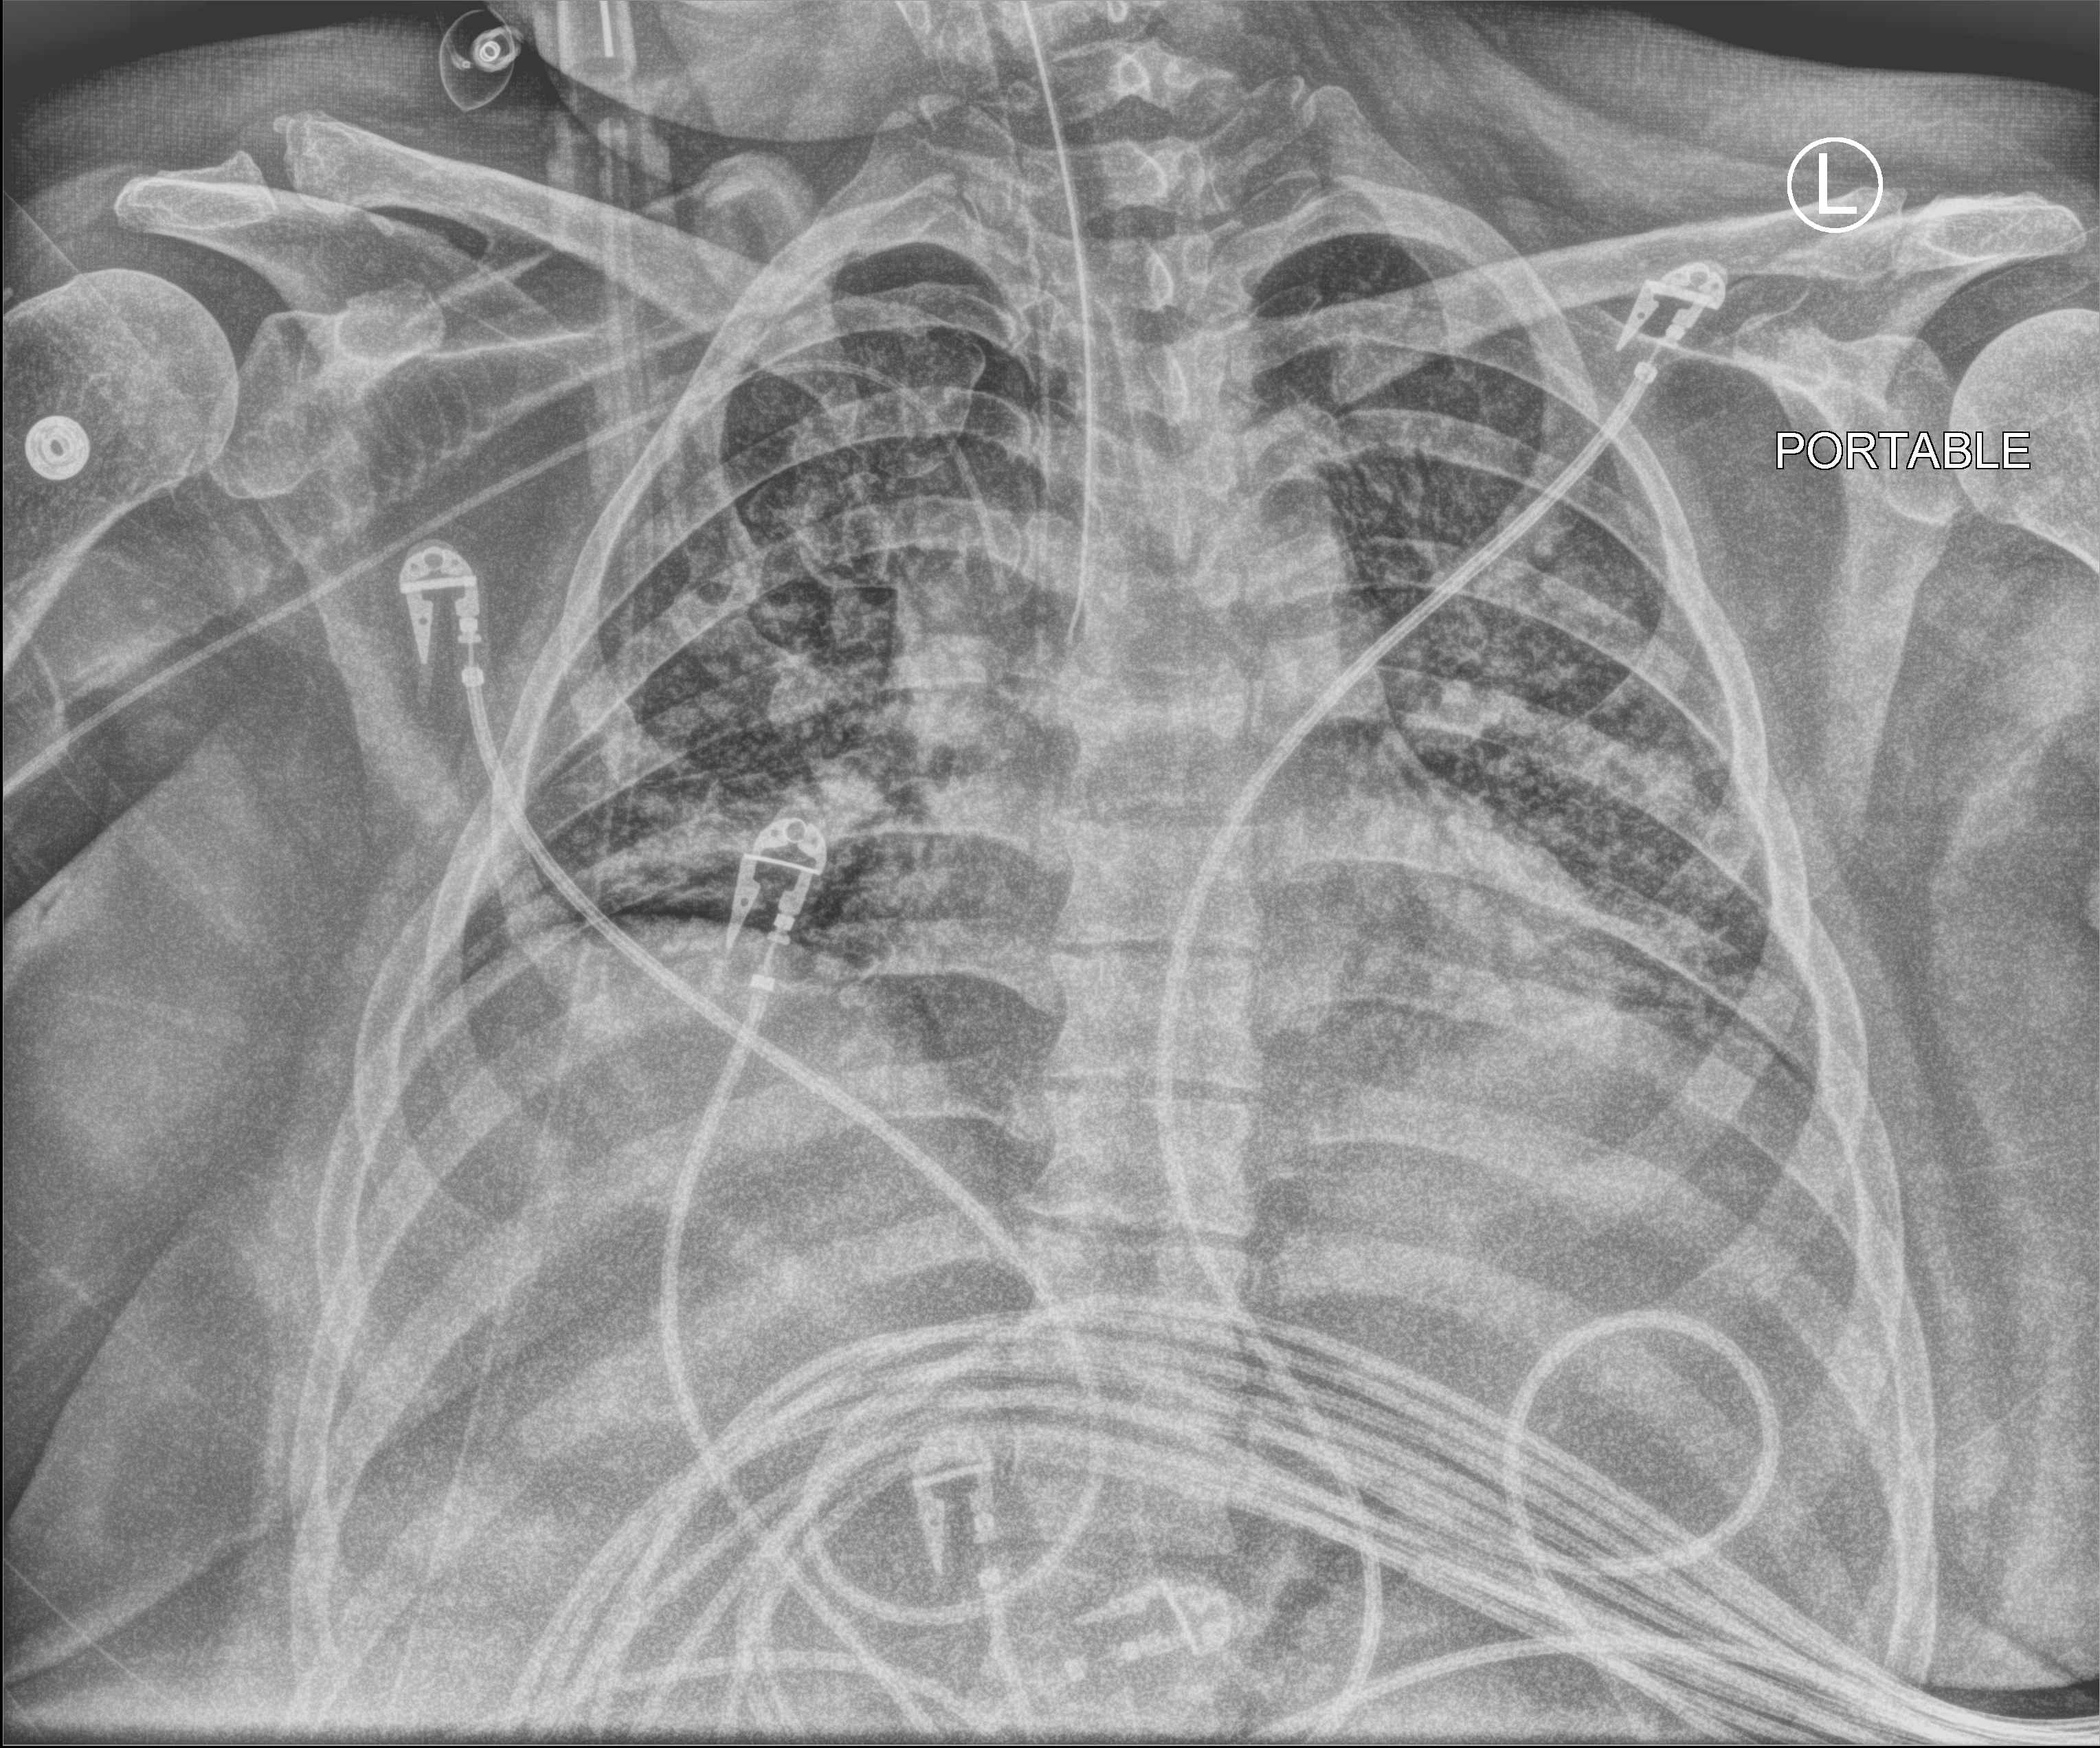
Bedside chest radiograph (computed radiography), anteroposterior (AP) projection. Patient hospitalised with COVID-19; female, aged 18–59 years.
From the hospital-stay record, not from the radiograph (when in the stay this image was taken is not recorded): COPD (admission record): no; mechanically ventilated during this hospital stay: yes.